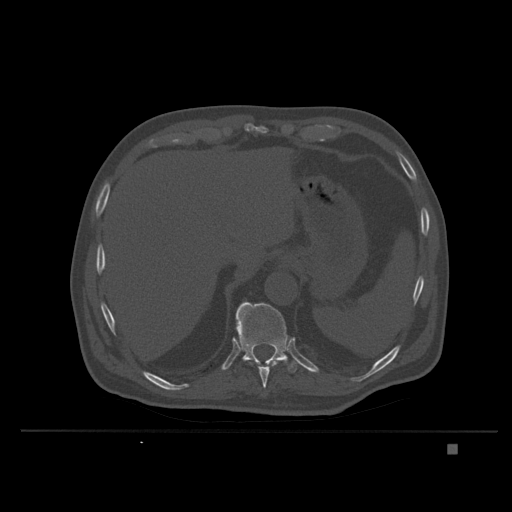
CT including the spine, one axial slice. Position 185 of 435 along the scan axis. Bone window (W 1800 / L 400 HU). 1.5 mm slice thickness. 512 × 512 image matrix. Male patient, age 73 years. From the clinical record (not read from this slice): primary cancer: skin.
Annotated regions visible in this slice (semi-automatic segmentation, software-assisted and operator-edited):
- T10 vertebra: bounding box <249,359,282,388> (left, top, right, bottom; pixels)
- T11 vertebra: <235,301,299,373>